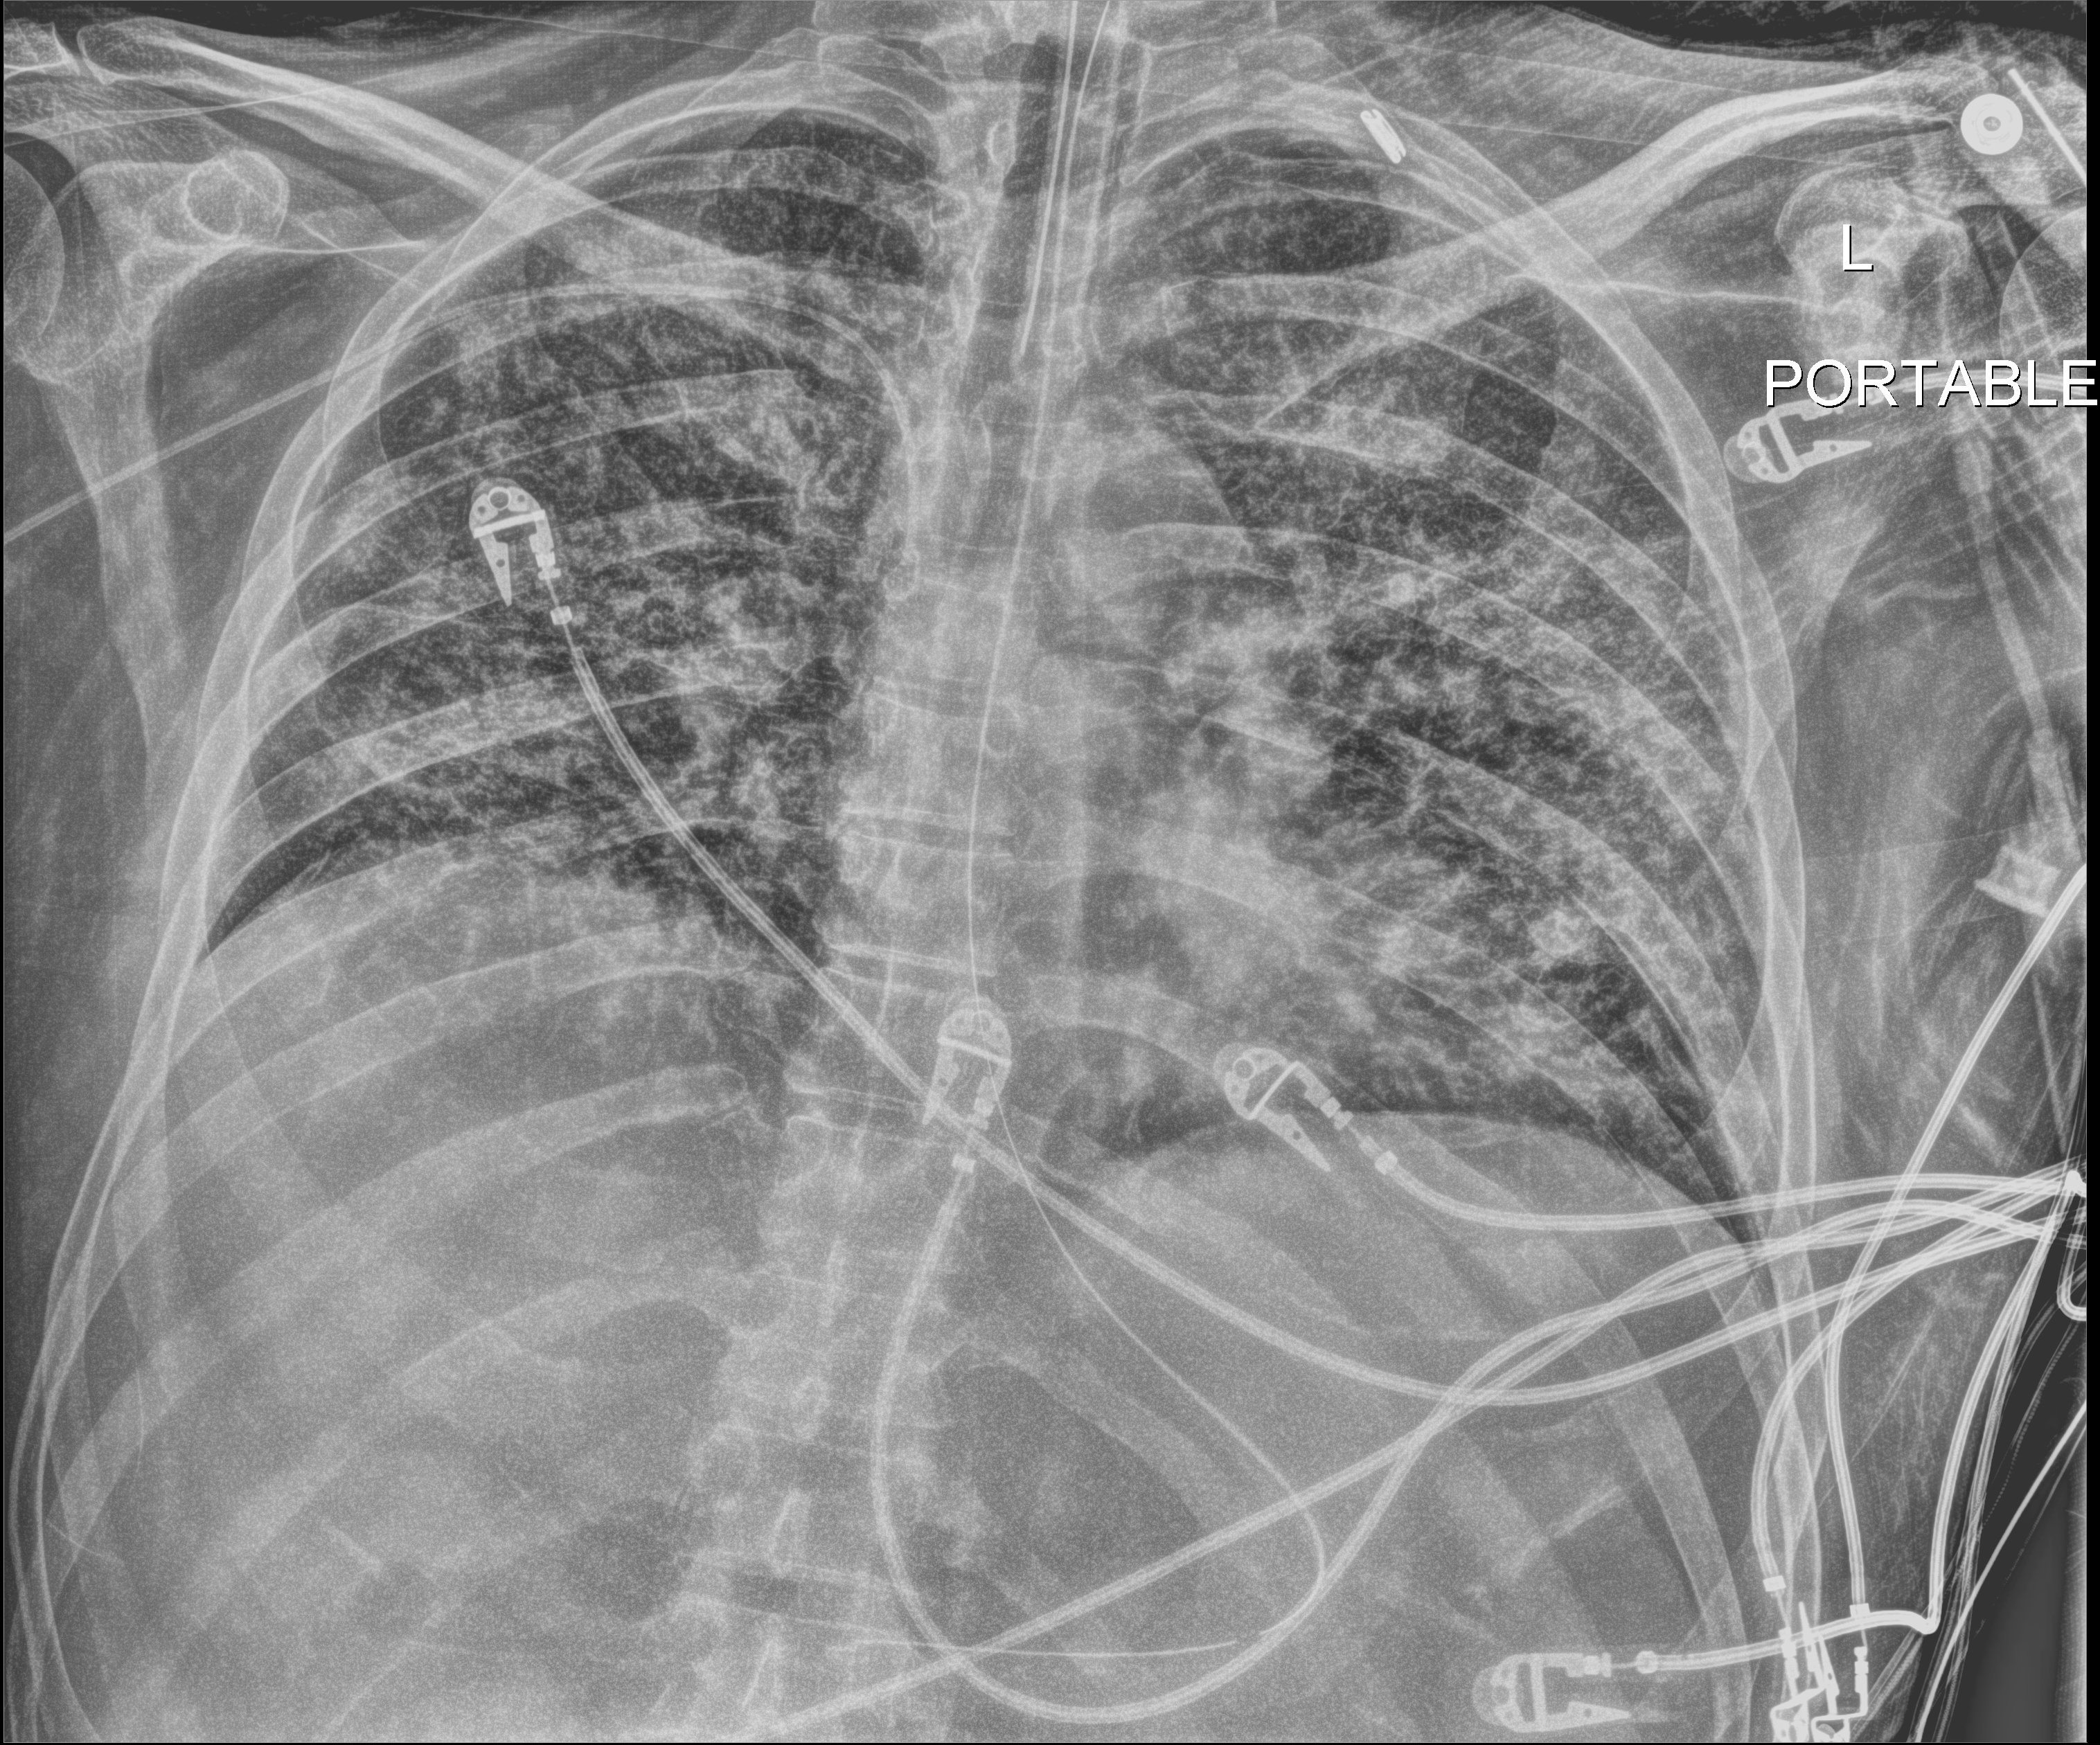
Portable chest radiograph, anteroposterior (AP) projection. Patient hospitalised with COVID-19; male, aged 18–59 years.
Hospital-stay facts (about this admission, not read from this image; timing relative to this image not recorded): admitted to intensive care during this hospital stay: yes; mechanically ventilated during this hospital stay: yes; length of hospital stay: 48 days.